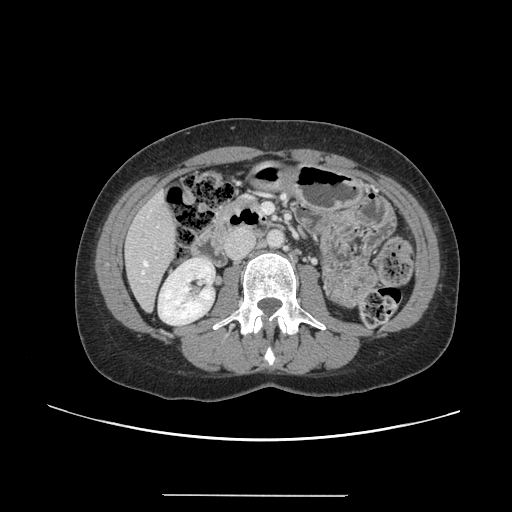
Contrast-enhanced abdominal CT, one axial slice; slice 43 of 144 in the series (ordered by position); 120 kVp; intravenous contrast given; soft-tissue window (W 400 / L 40 HU); 512 × 512 image matrix. Female patient, age 53 years. Case-level facts recorded for this patient, not image findings: diagnosis: colorectal cancer liver metastases, imaged before liver resection; multiple liver metastases: yes; largest metastasis: 1.1 cm; chemotherapy before resection: no.
Outlined on this slice (expert manual segmentation):
- hepatic veins: box from (x=142, y=261) to (x=148, y=274) px
- liver: (x=125, y=195)–(x=177, y=309)
- planned liver remnant (the part of the liver to remain after resection): (x=126, y=195)–(x=177, y=309)